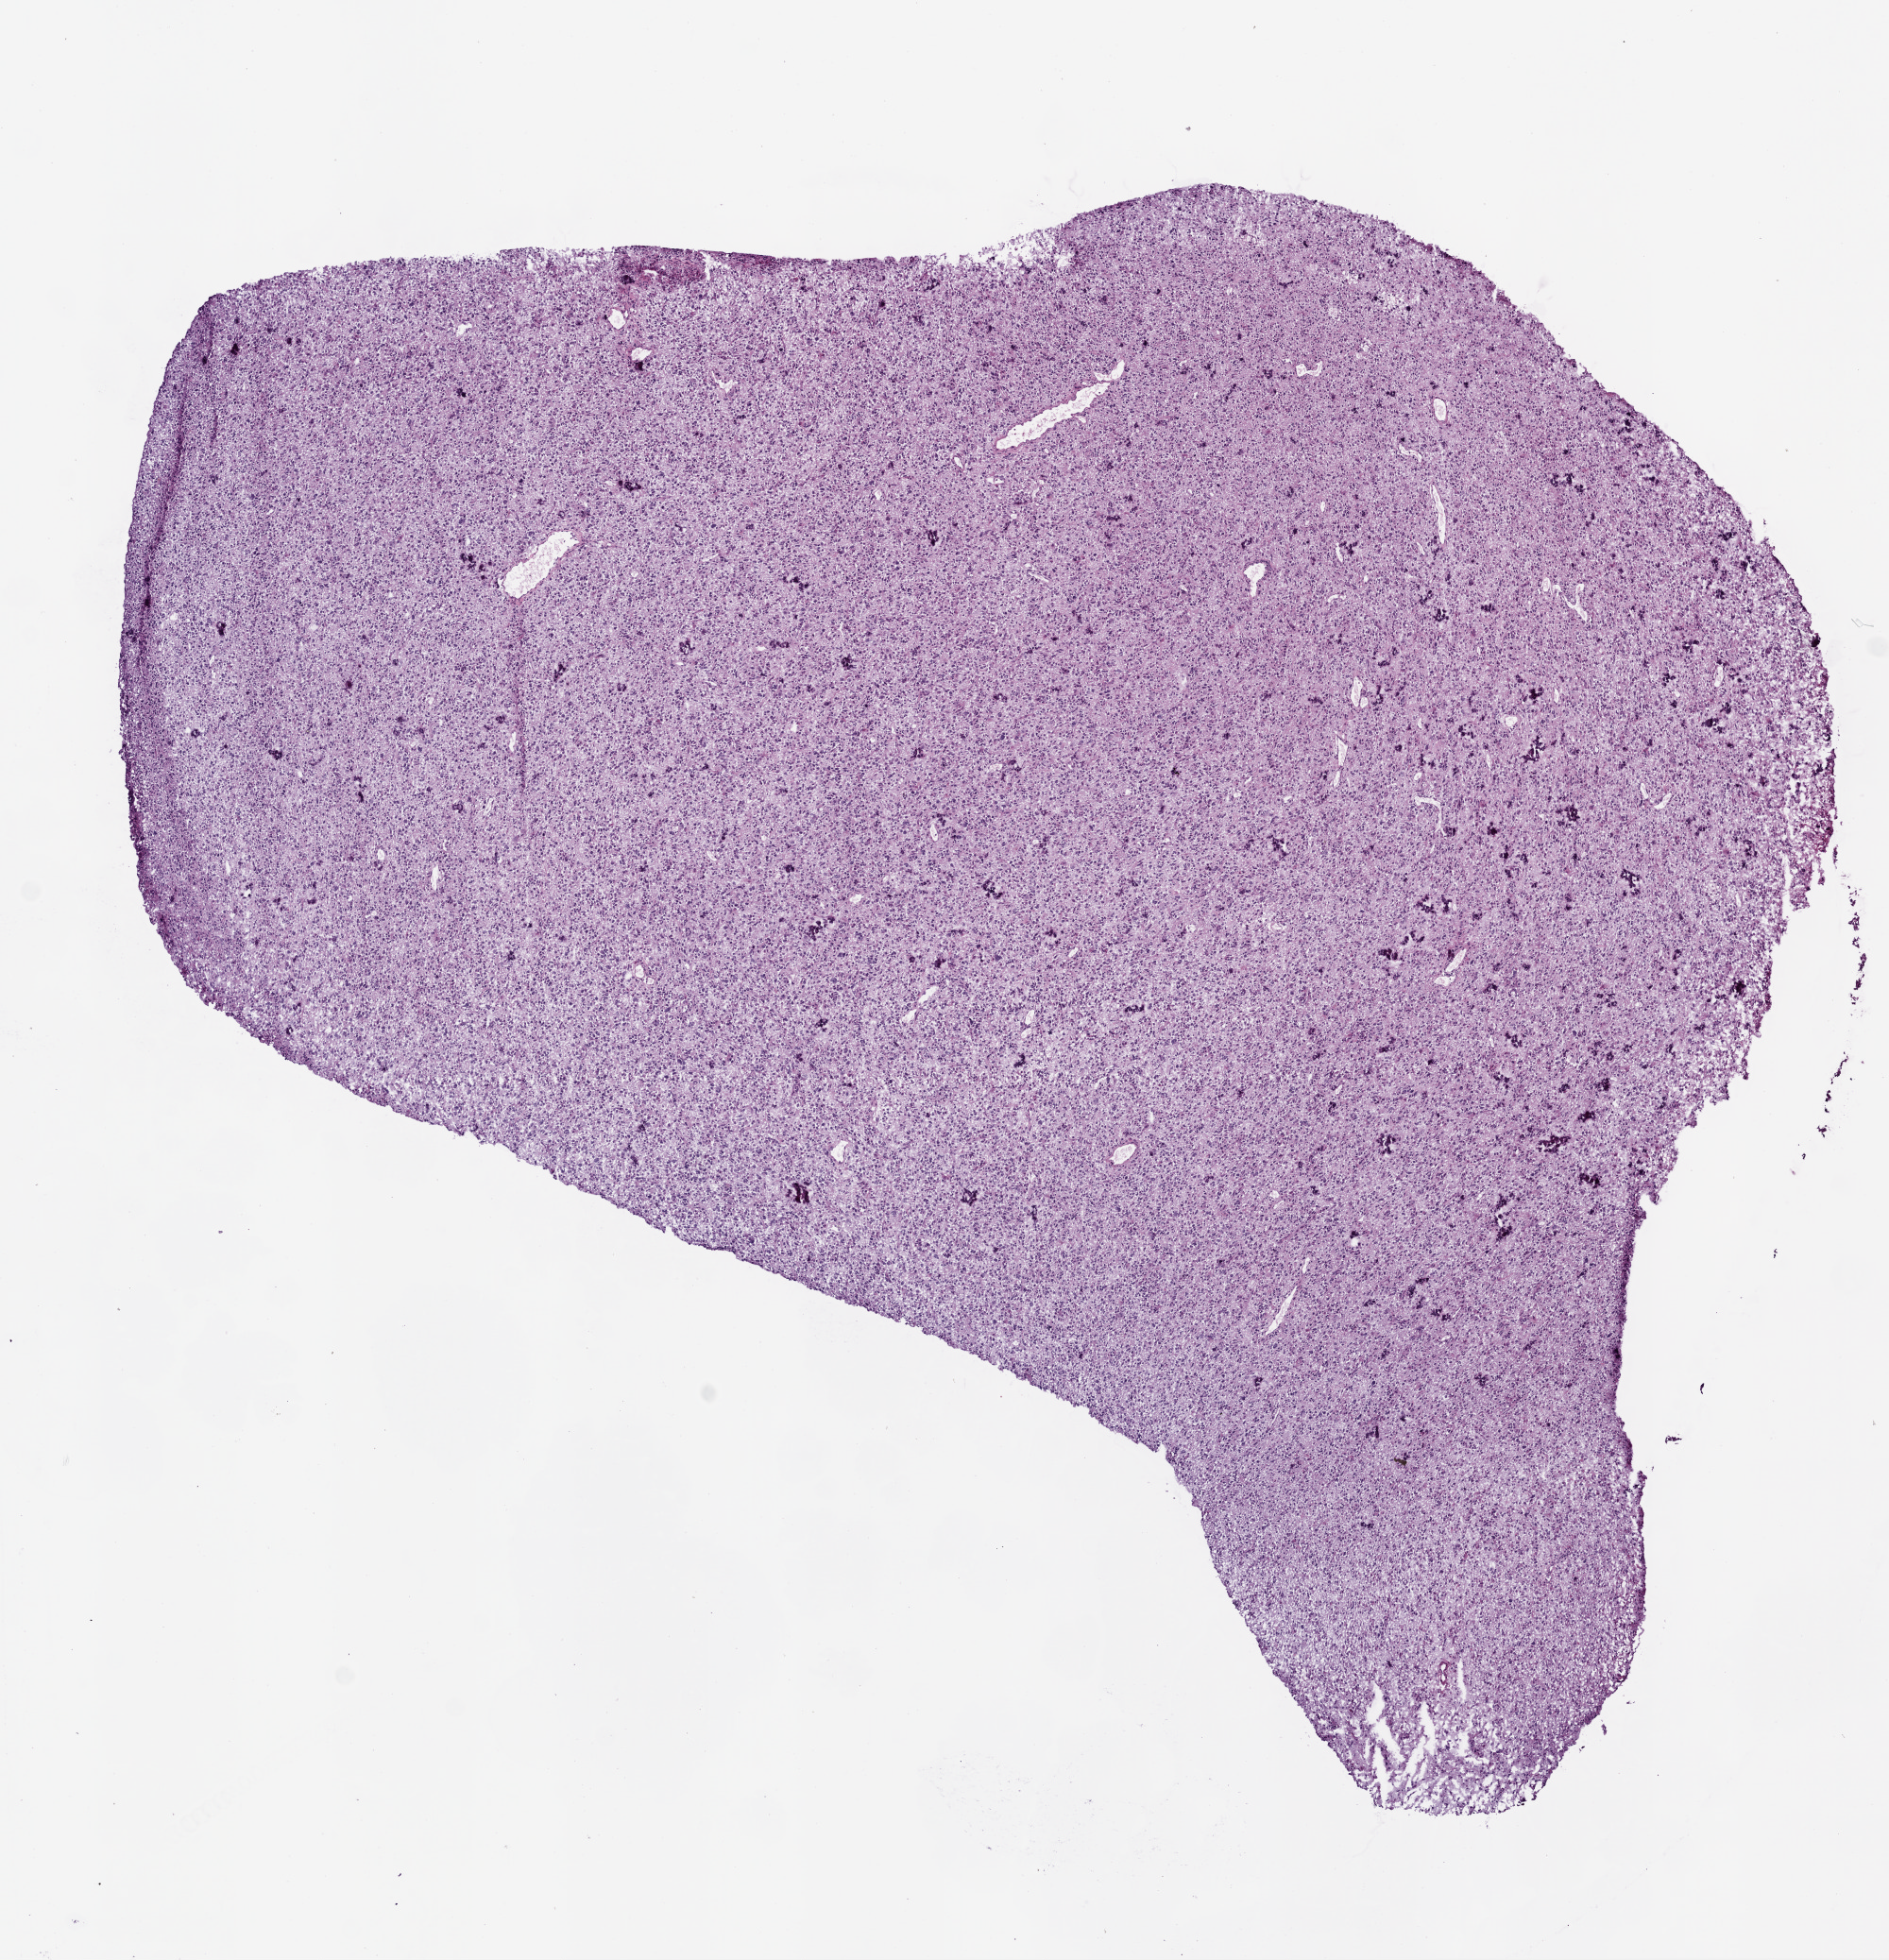
Whole-slide histology image, Hematoxylin and eosin (H&E) stained — shown as a low-resolution overview of the whole scanned area (about 8.0 x 8.3 mm, acquisition: 20x scan), frozen section from the bottom of the tissue portion, primary tumour sample from the brain. Male patient; age at initial diagnosis 71 years. Composition of this section per pathologist review: tumour cells 100%, tumour nuclei 80%, normal cells 0%, stromal cells 0%, necrosis 0%.
Diagnosis: Glioblastoma.